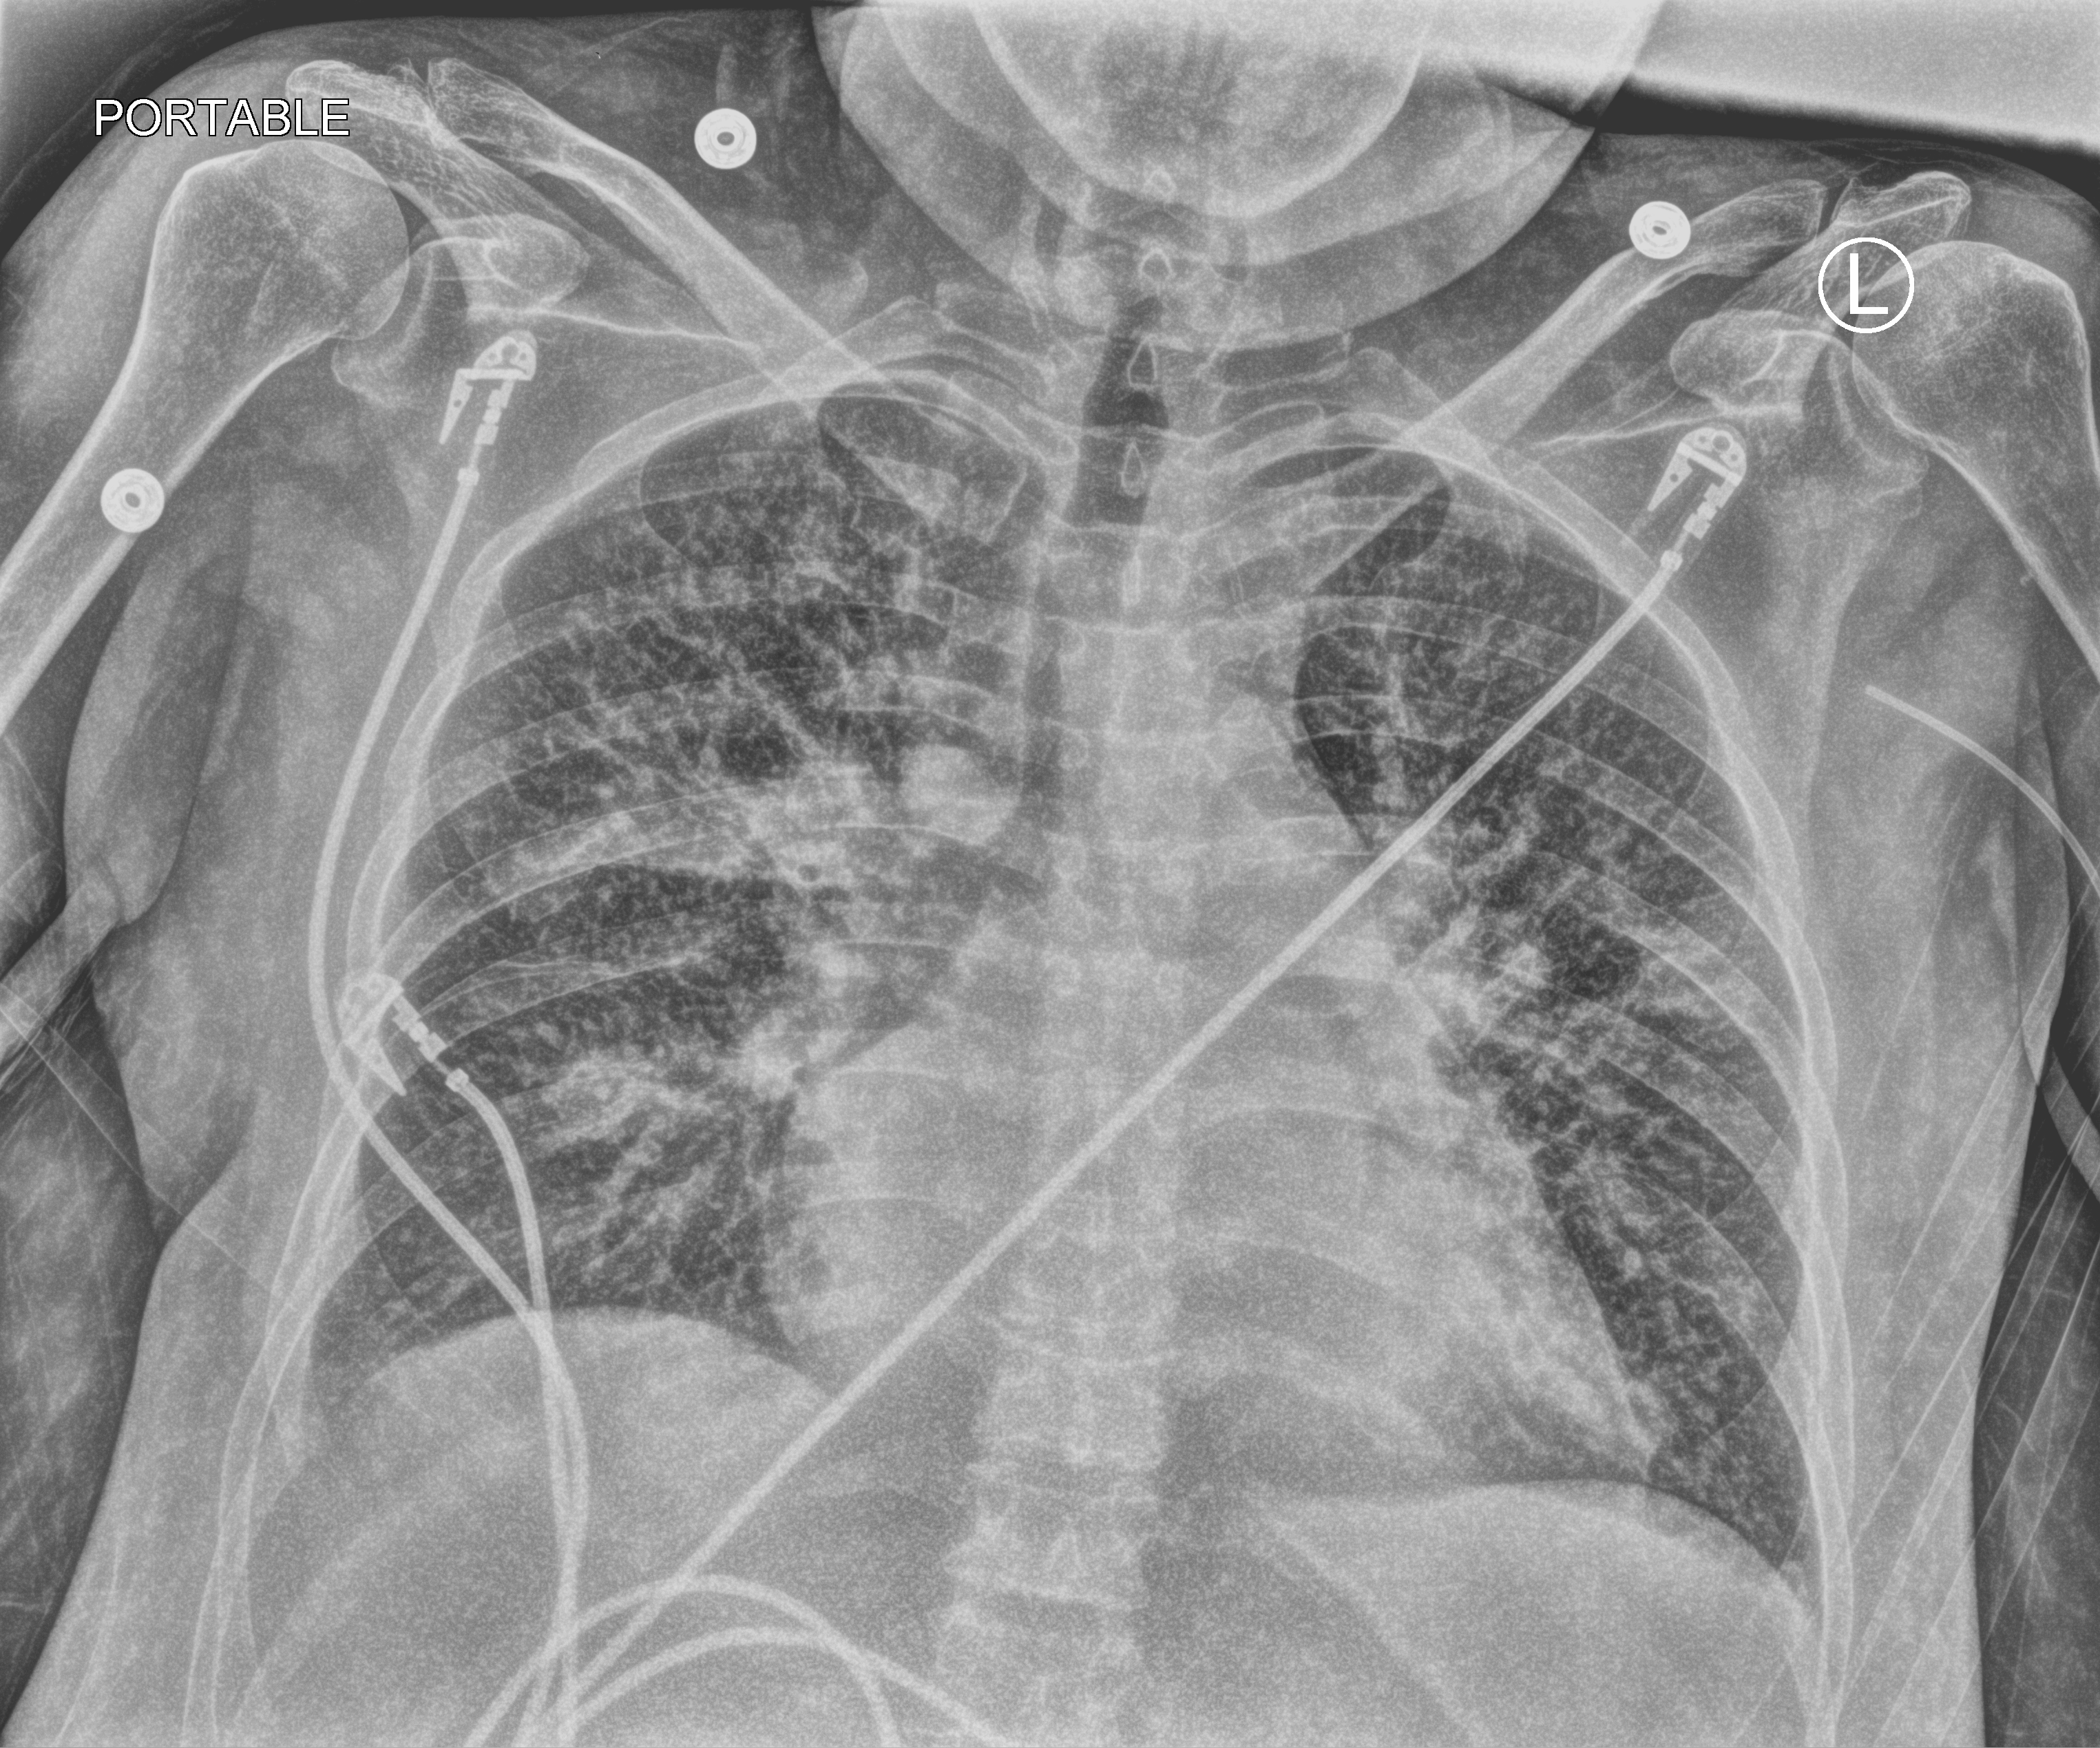
Portable chest radiograph, anteroposterior (AP) projection. Patient hospitalised with COVID-19; female, aged 18–59 years.
Hospital-stay facts (about this admission, not read from this image; timing relative to this image not recorded):
- mechanically ventilated during this hospital stay: no
- hypertension (admission record): no